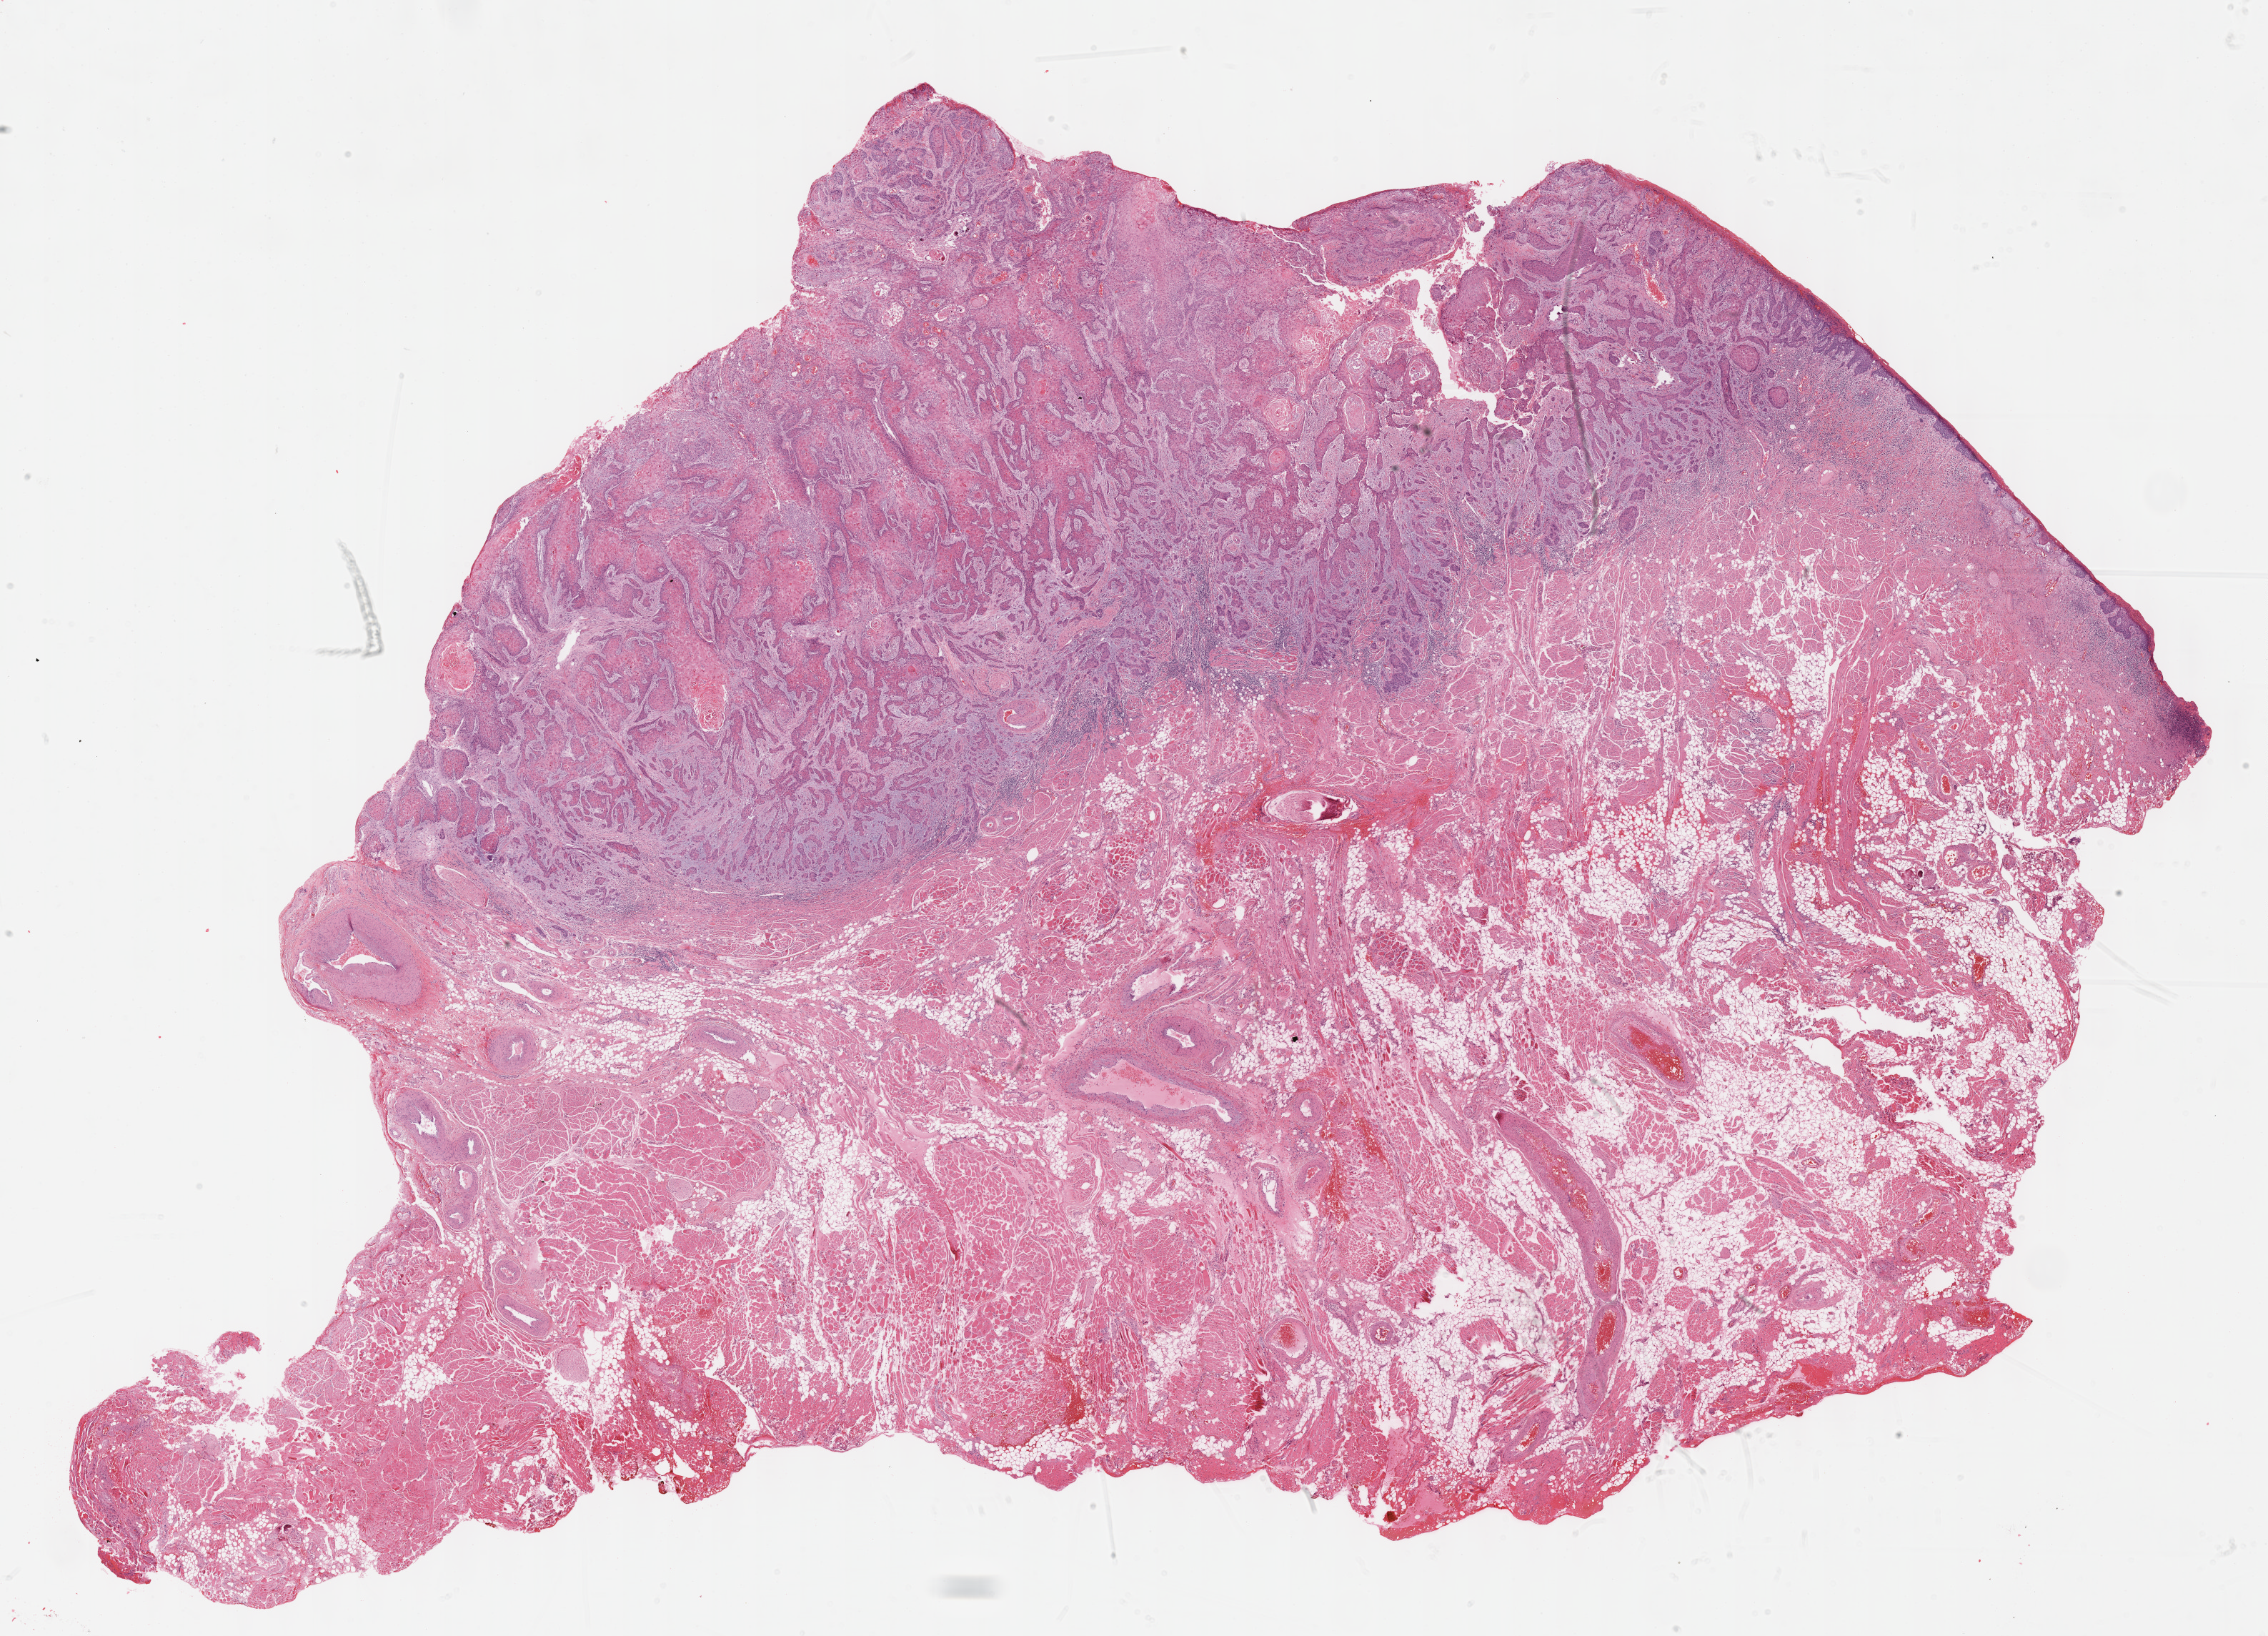
H&E-stained whole-slide image, shown as a low-resolution overview of the whole scanned area (about 25.7 x 18.5 mm, acquisition: 40x scan); formalin-fixed paraffin-embedded (FFPE) diagnostic section; sample: primary tumour, head and neck. Patient: female, age at initial diagnosis 77 years. Histologic grade: G3 (poorly differentiated).
AJCC pathologic stage: IVA. Pathologic diagnosis: Squamous cell carcinoma, NOS (tongue, NOS). Laterality: left. Lymph nodes positive (case pathology): 6 of 34 examined.